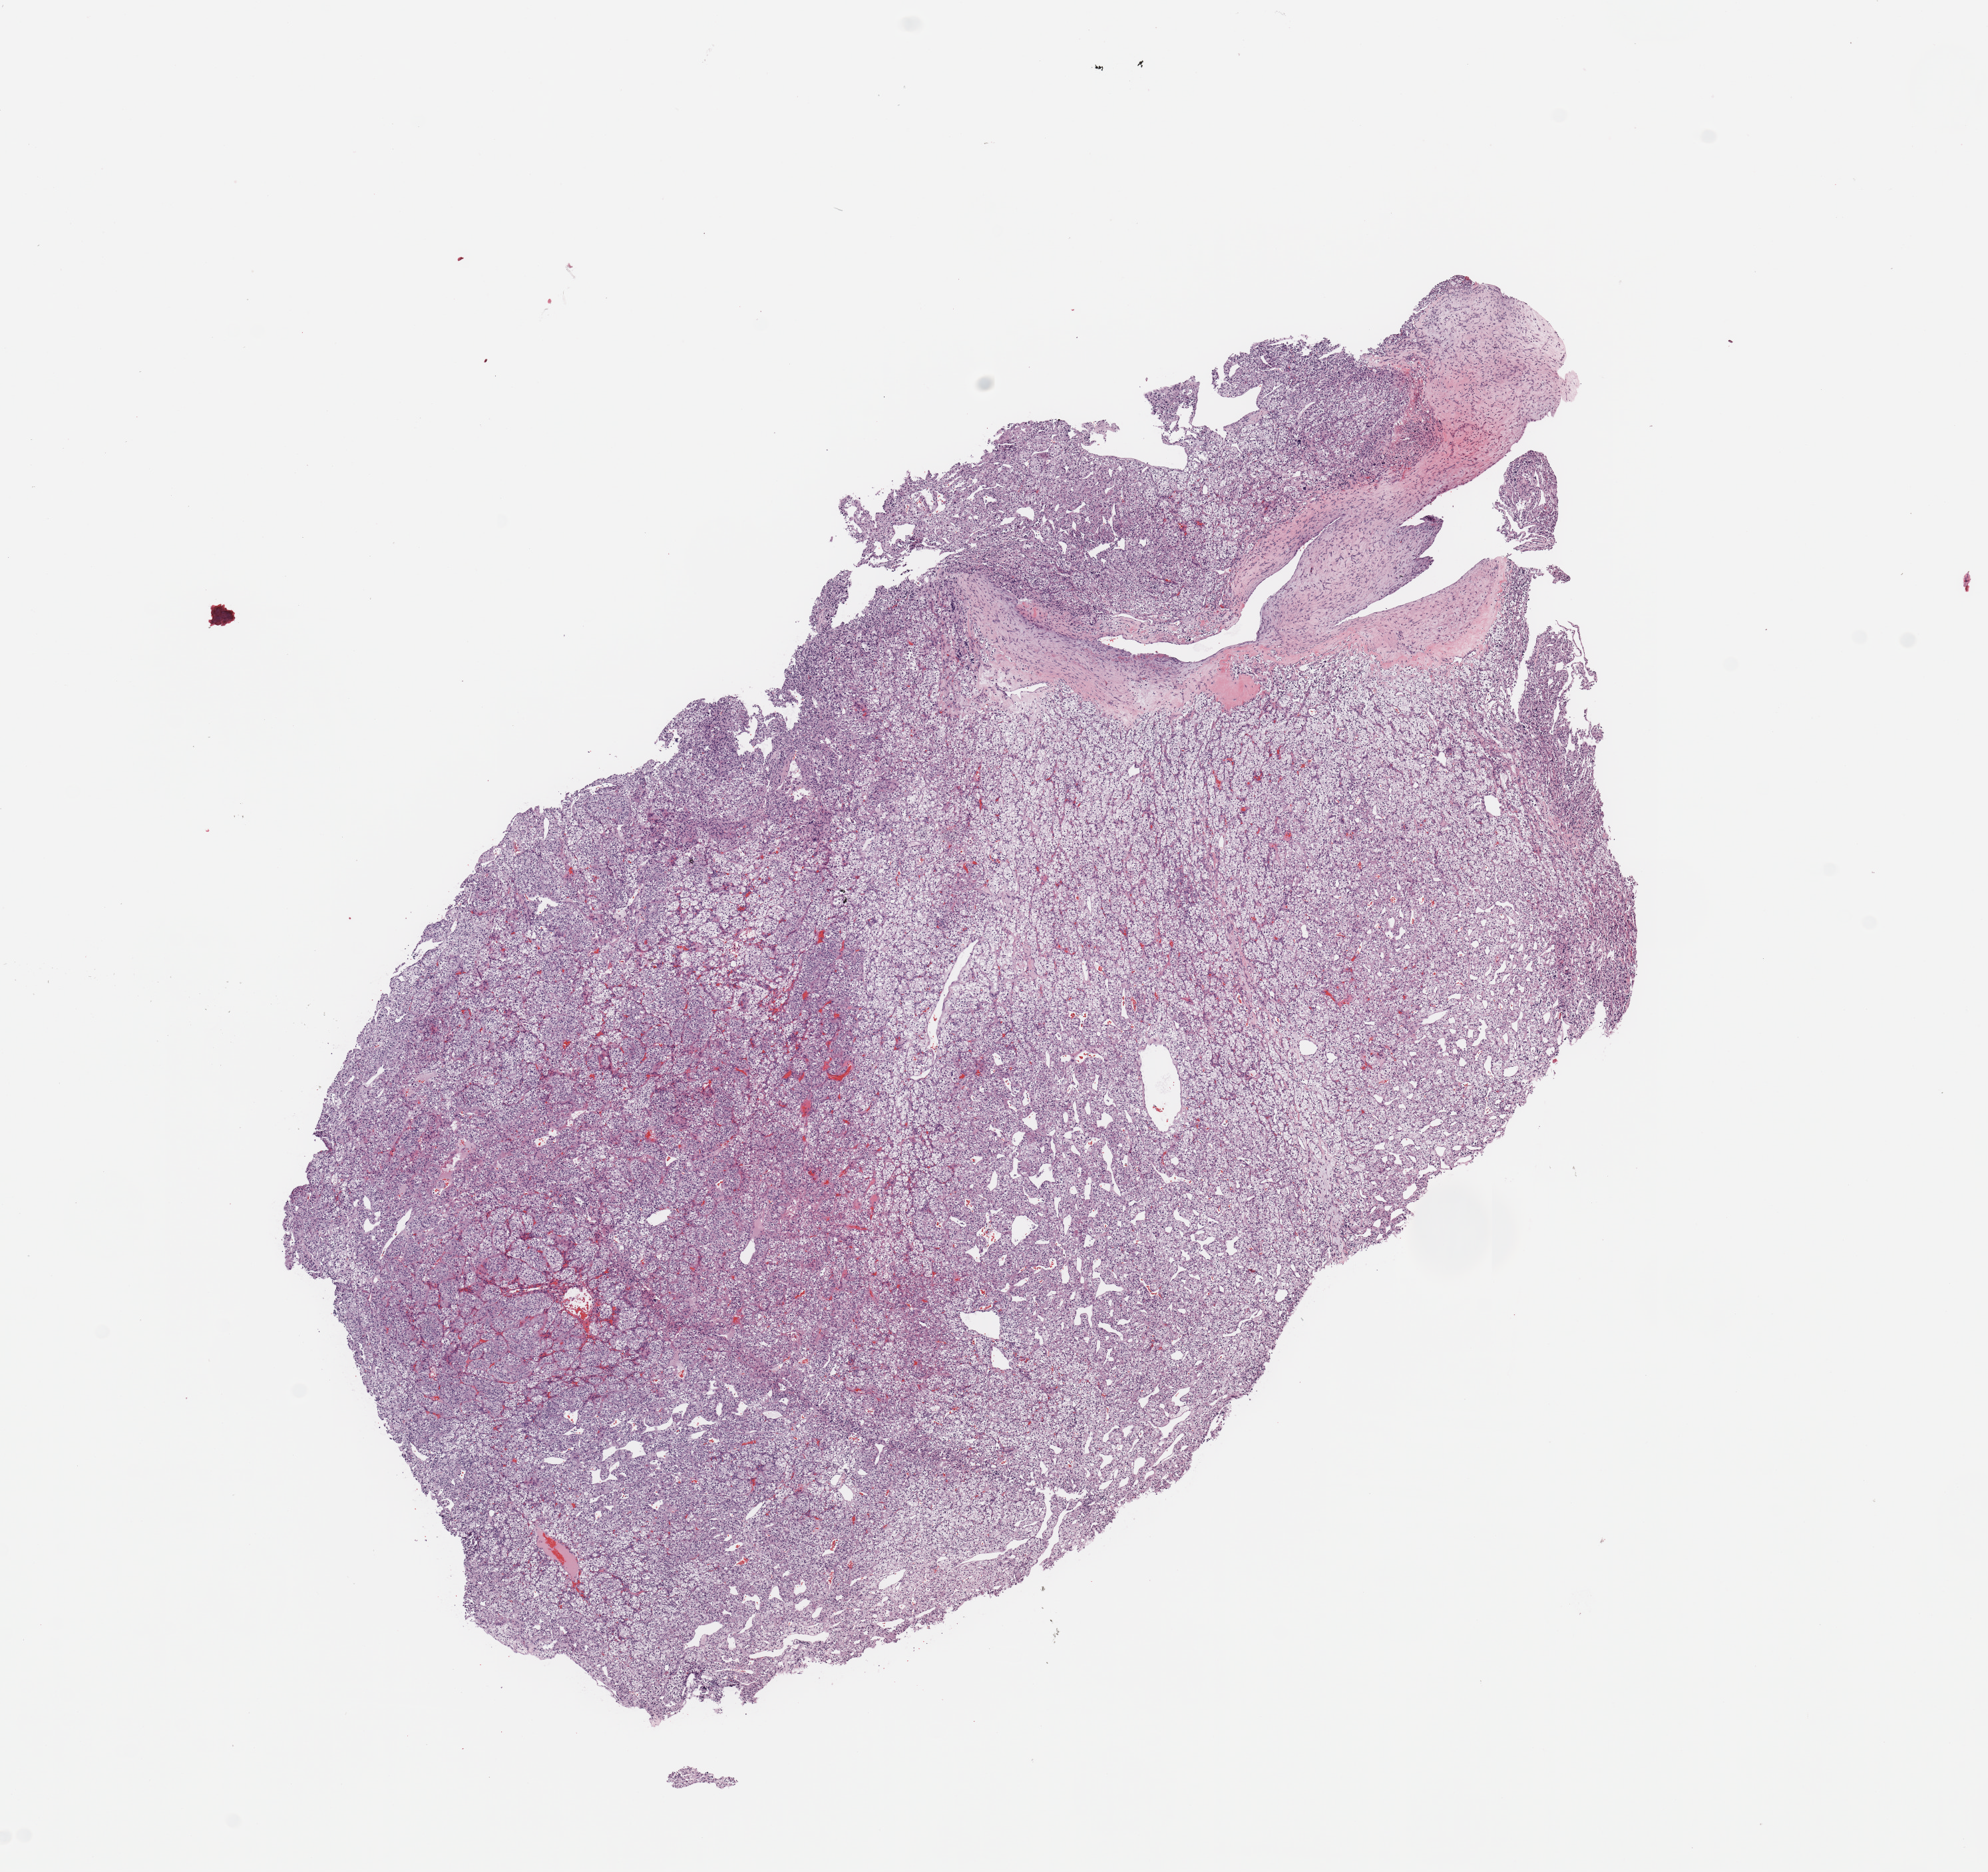
Digitized Hematoxylin and eosin (H&E) stained tissue section (whole slide), whole scanned area (about 11.8 x 11.1 mm, from a 20x scan) shown as a low-resolution overview. Tumour tissue sample, sampled site: kidney. Female, 63 y/o.
Diagnosis: Renal cell carcinoma, NOS.